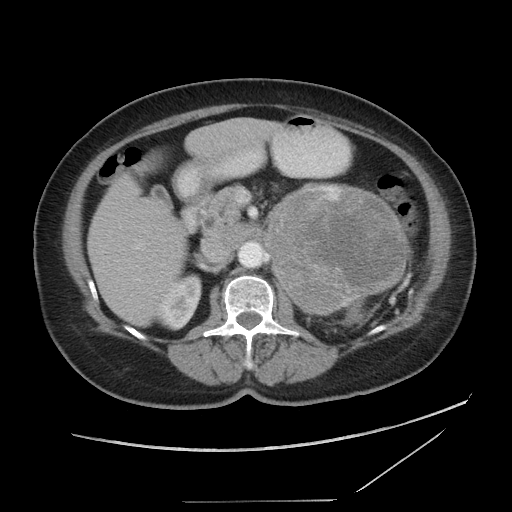
Contrast-enhanced abdominal CT, one axial slice. Position 53 of 86 along the scan axis. Reconstruction kernel STANDARD. 120 kVp. Intravenous contrast given. Soft-tissue window (W 400 / L 40 HU). 5 mm slice thickness. 512 × 512 image matrix, field of view 398 × 398 mm. Female patient, age 77 years. From the clinical record (not read from this slice): diagnosis: adrenocortical carcinoma; tumour side: left adrenal; tumour size at pathology: 13.1 cm; Ki-67 index: 10 %; stage (as recorded): 3.
Outlined on this slice (semi-automatically segmented with operator editing):
- mass: bounding box [x1, y1, x2, y2] px = [267, 185, 406, 313]